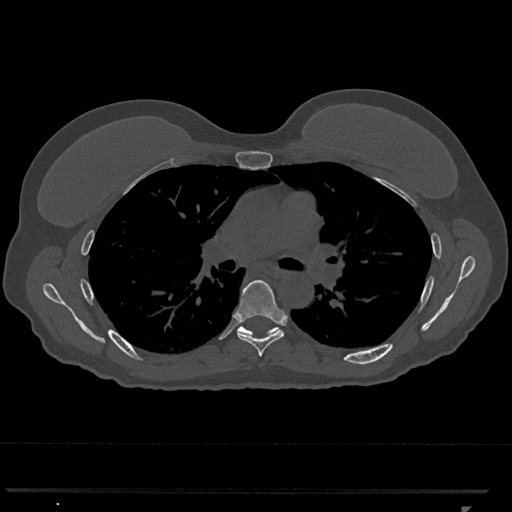
CT including the spine, one axial slice; slice 751 of 793 in the series (ordered by position); reconstruction kernel Br40s/3; 120 kVp; bone window (W 1800 / L 400 HU); 512 × 512 image matrix, field of view 380 × 380 mm. Patient: female, 62 years. Case-level facts recorded for this patient, not image findings: primary cancer: renal.
Outlined on this slice (semi-automatically segmented with operator editing):
- T6 vertebra: bounding box [x1, y1, x2, y2] px = [237, 279, 285, 357]
- T7 vertebra: [237, 323, 279, 336]